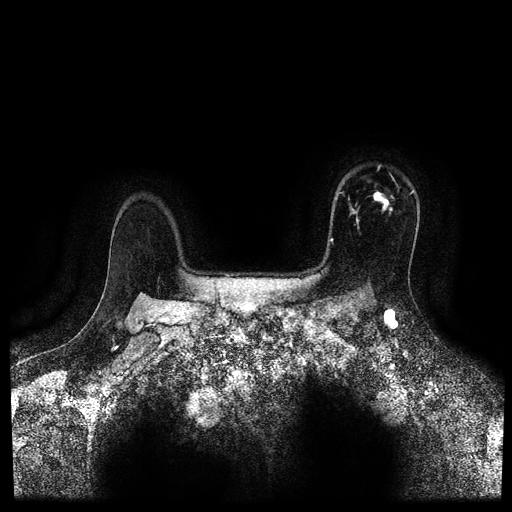
Breast MRI (dynamic contrast-enhanced, multi-phase), one axial slice; dynamic contrast-enhanced series, time point 2 of 5 at this slice position (early post-contrast); 1.5 T; TE 2.7 ms, TR 5.4 ms; 512 × 512 image matrix, field of view 340 × 340 mm. Patient: female, 50 years.
Structures marked on this image (semi-automatically segmented with operator editing):
- breast lesion (labelled 'tumour' in the annotation; benign lesions carry a separate 'benign' label): bounding box [x1, y1, x2, y2] px = [368, 188, 395, 218]